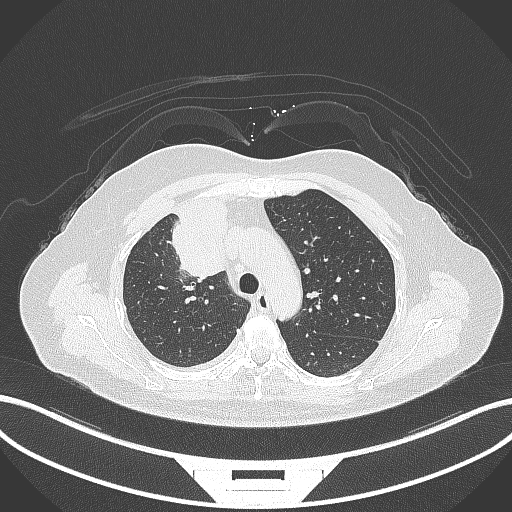
Chest CT, one axial slice. Slice 213 of 305 in the series (ordered by position). Reconstruction kernel B70f. Lung window (W 1500 / L -600 HU). 1 mm slice thickness. 512 × 512 image matrix, field of view 400 × 400 mm. Patient: female, 52 years. Case-level facts recorded for this patient, not image findings: clinical TNM (as recorded): T3 N1 M1.
Outlined on this slice (rectangle marked by the reading radiologist):
- lung tumour (recorded histology: adenocarcinoma): bounding box [x1, y1, x2, y2] px = [164, 198, 233, 283]